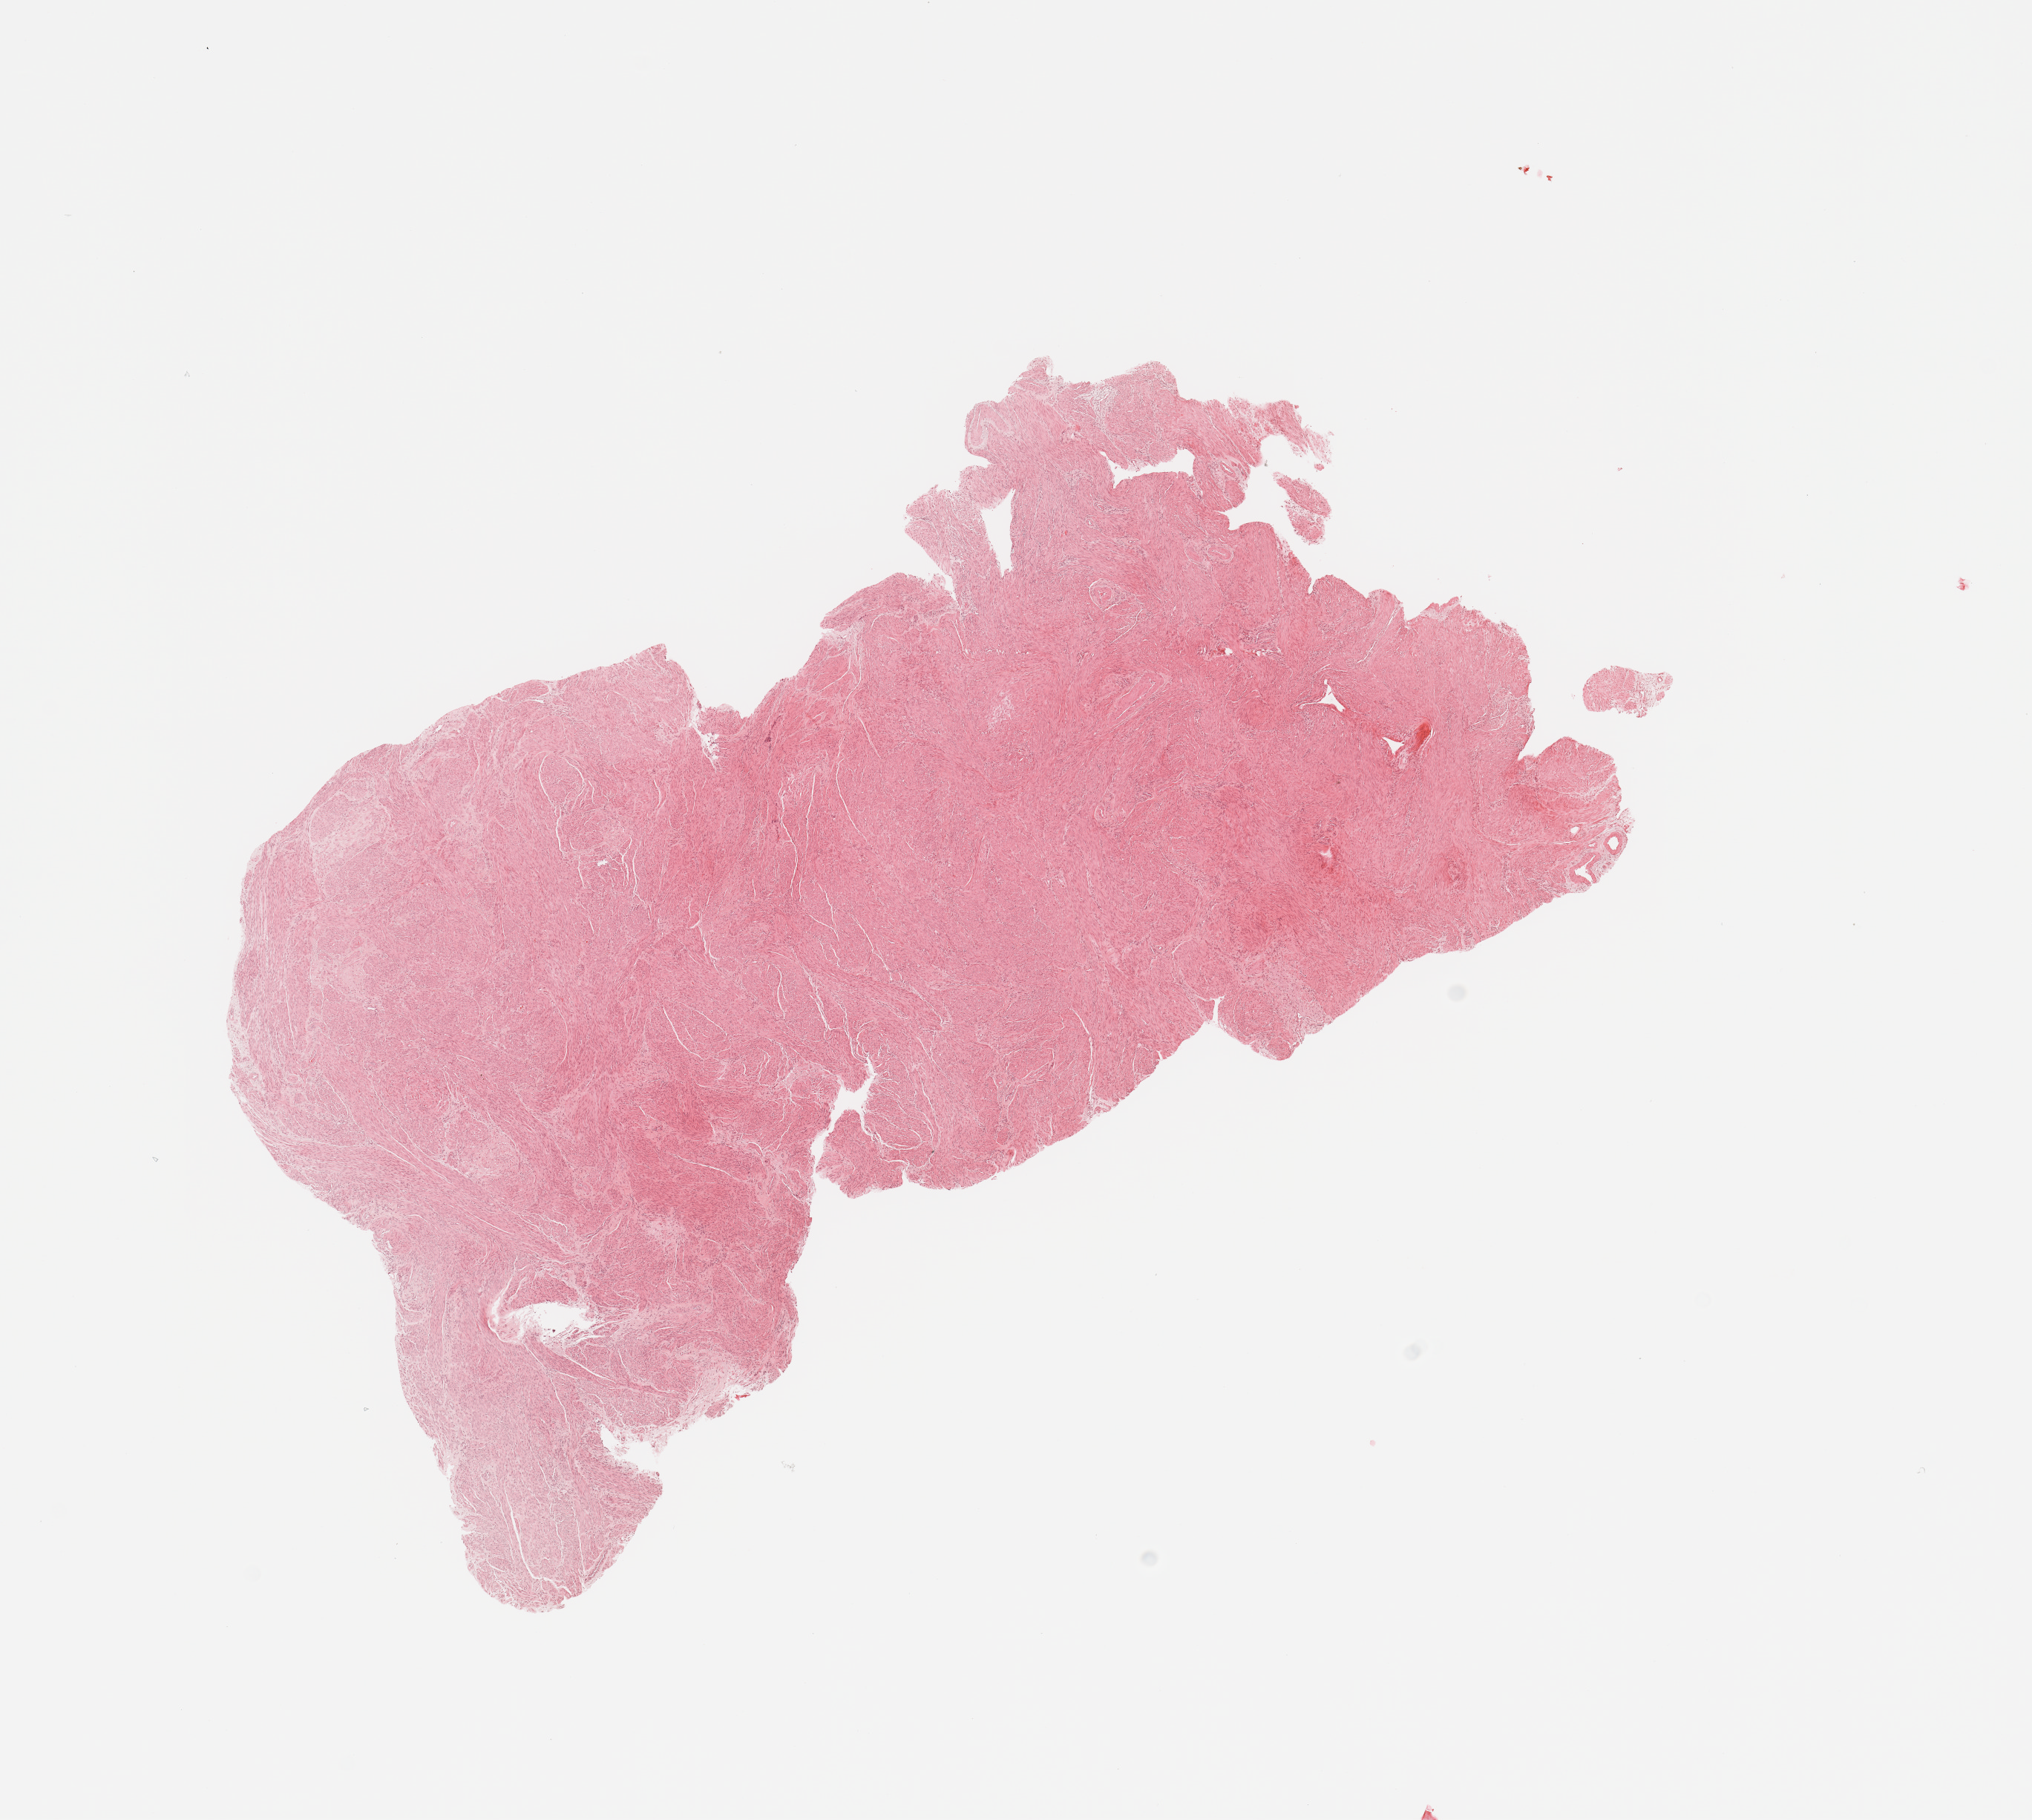
Whole-slide histology image, H&E-stained — a low-resolution overview of the entire scanned area, about 10.8 x 9.7 mm (slide scanned at 20x), uterus, normal (non-tumour) tissue. Female, 73 y/o.
This section: normal (non-tumour) tissue from the same patient. Patient diagnosis: Endometrioid adenocarcinoma, NOS.